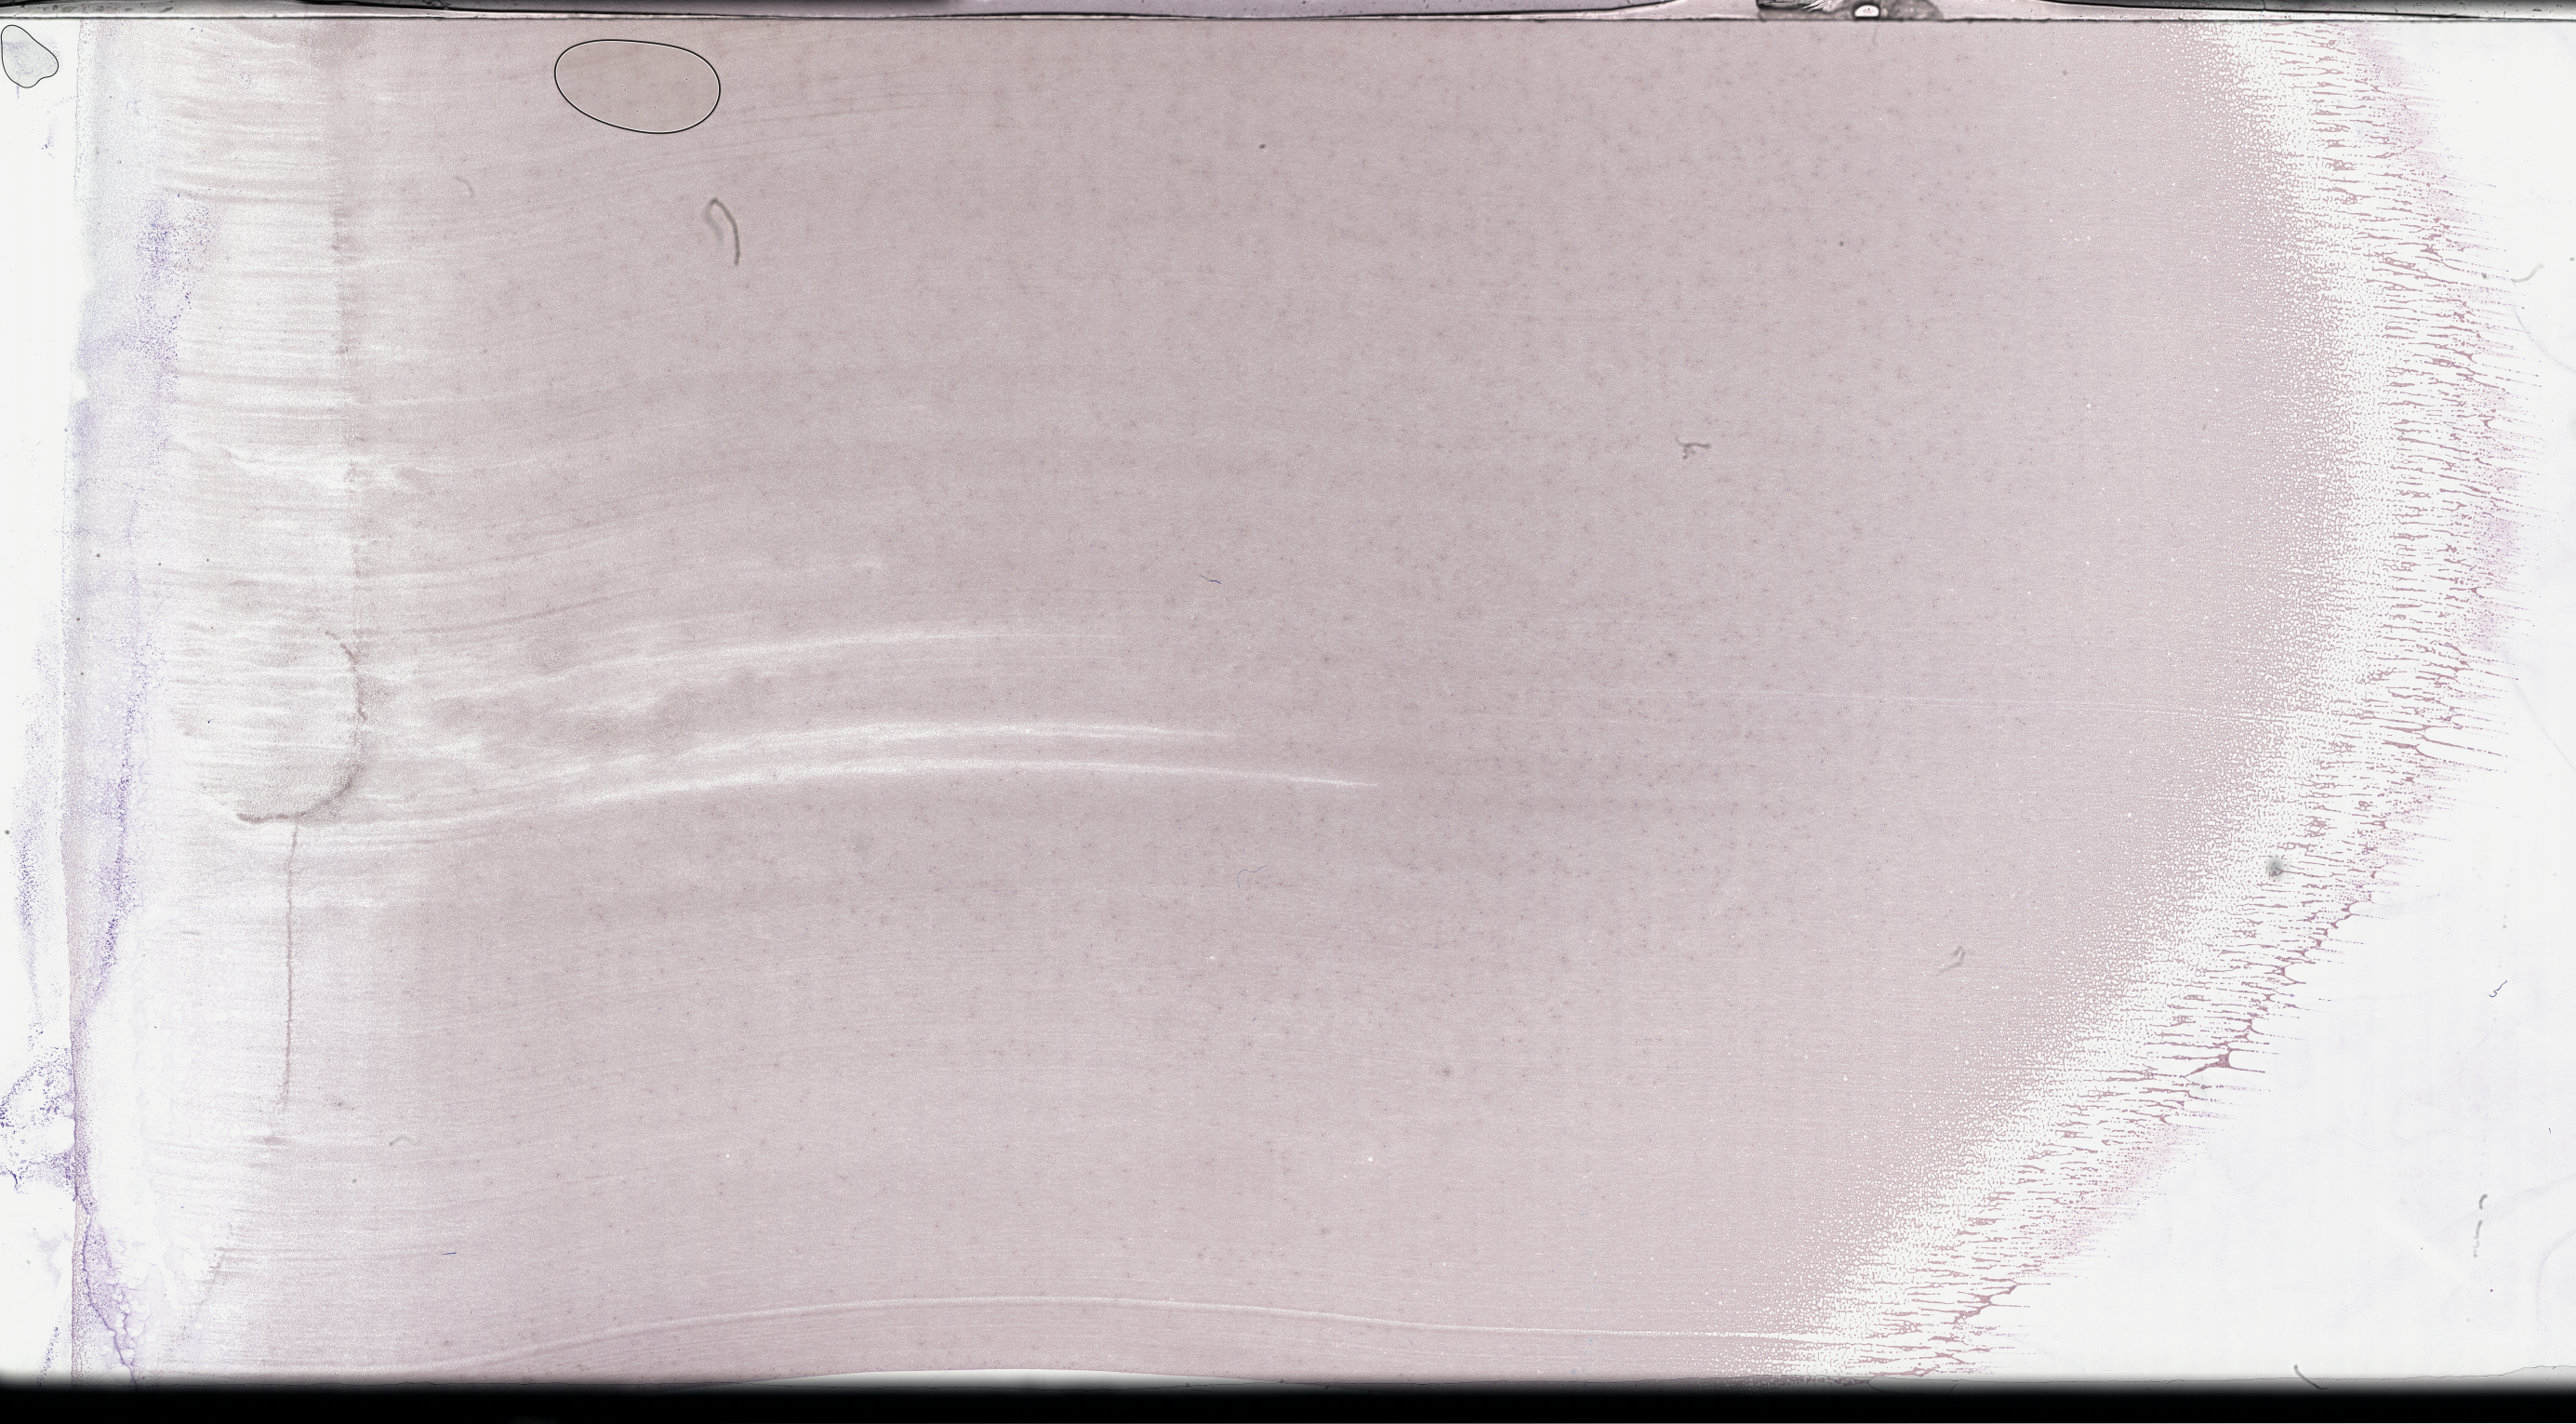
Whole-slide image of a whole blood smear, Wright–Giemsa stain, low-resolution overview of the scanned area, about 44.7 x 24.7 mm, specimen time point: collected on treatment. Female patient.
Patient diagnosis: Plasma Cell Myeloma.